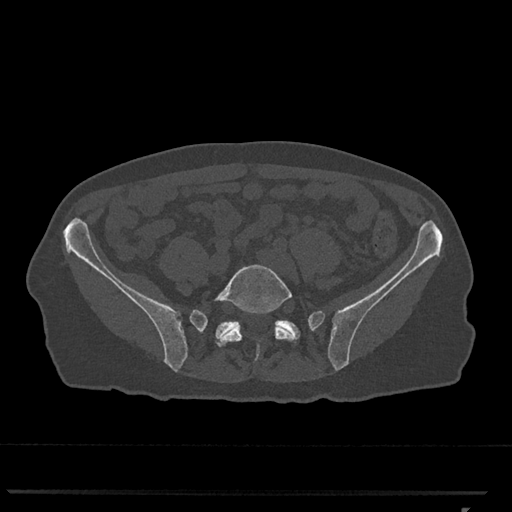
CT including the spine, one axial slice; position 135 of 793 along the scan axis; reconstruction kernel Br40s/3; 120 kVp; bone window (W 1800 / L 400 HU); 0.5 mm slice thickness; 512 × 512 image matrix, field of view 380 × 380 mm. Patient: female, 62 years. Case-level facts recorded for this patient, not image findings: primary cancer: renal.
Outlined on this slice (semi-automatically segmented with operator editing):
- L5 vertebra: bounding box [x1, y1, x2, y2] px = [214, 264, 297, 361]